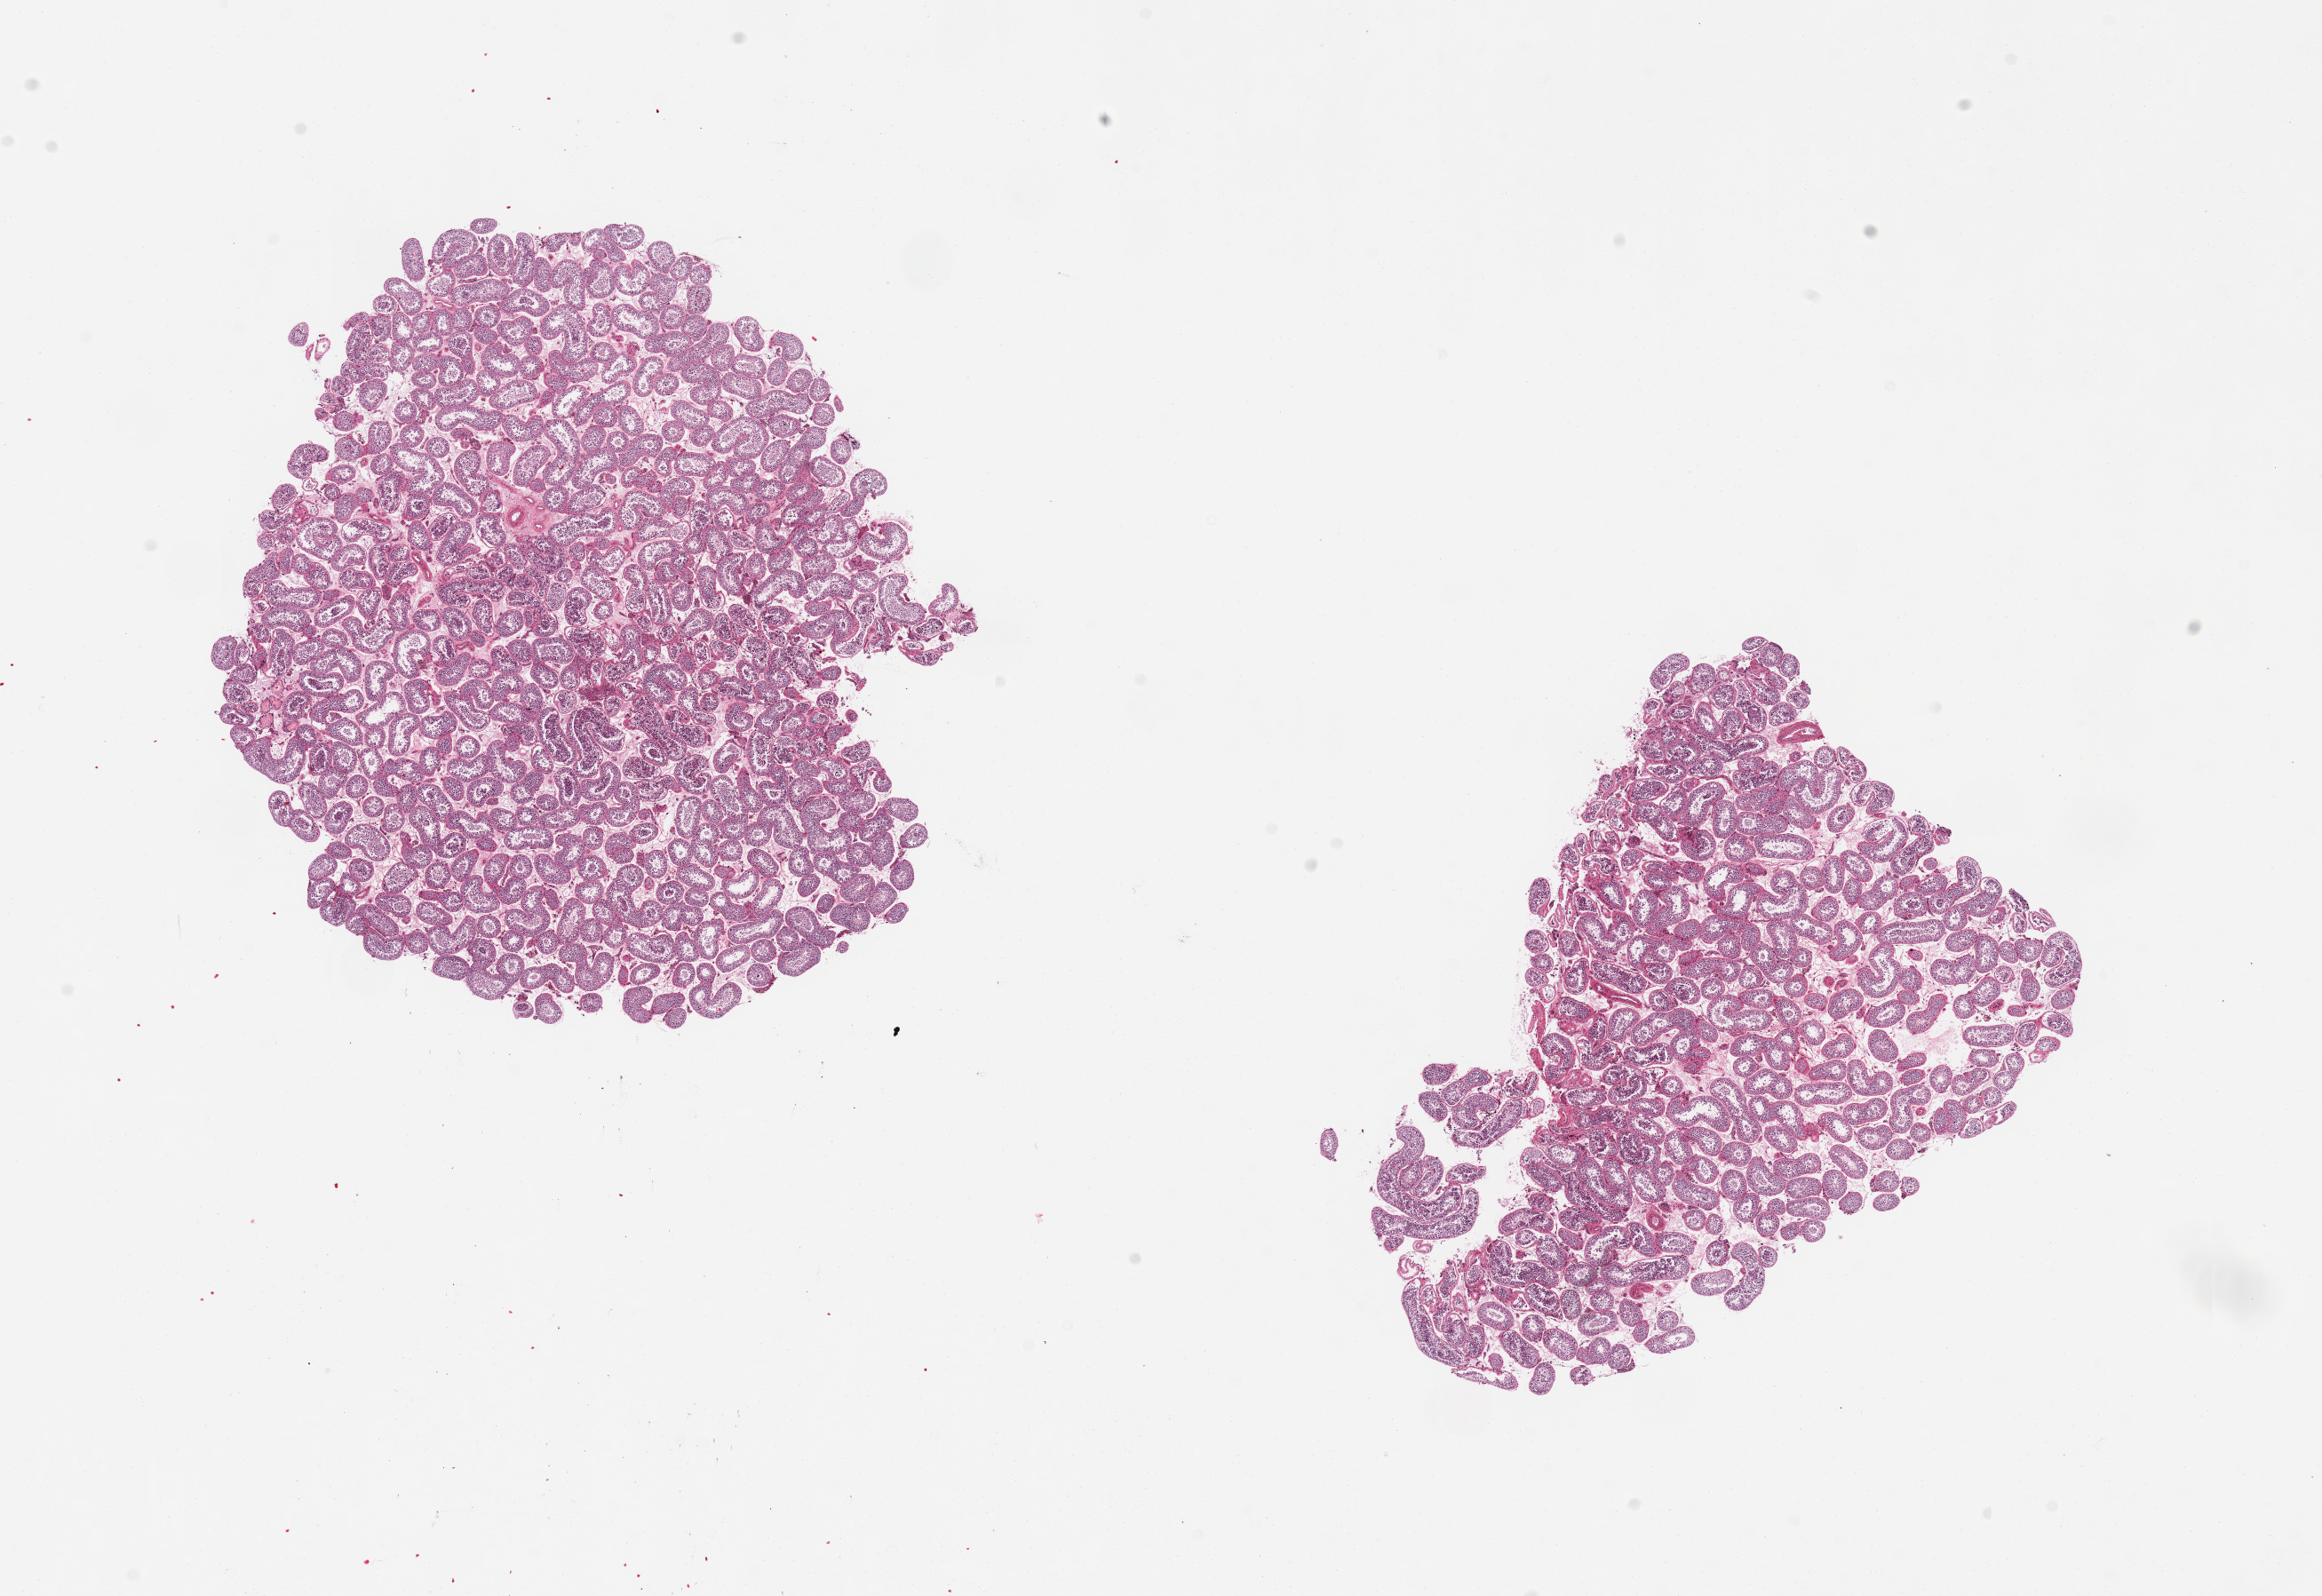
Digitized H&E-stained section — a low-resolution overview of the entire scanned area, about 20.7 x 14.2 mm, PAXgene-fixed paraffin-embedded (PFPE) section, target tissue: testis, donor tissue sample. Donor: male.
• review note (as recorded): 2 pieces, spermatogenesis is present